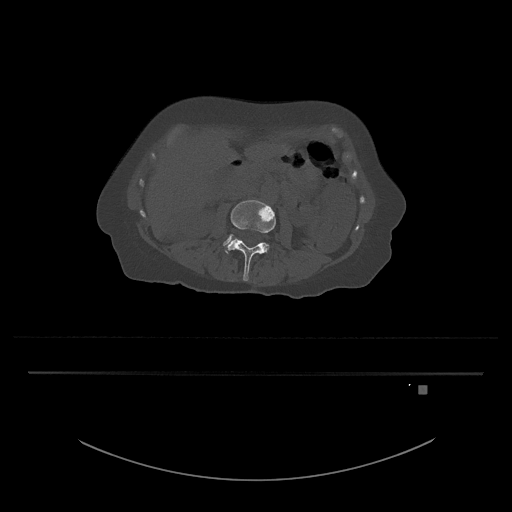
CT including the spine, one axial slice. Slice 419 of 797 in the series (ordered by position). 120 kVp. Bone window (W 1800 / L 400 HU). 0.5 mm slice thickness. 512 × 512 image matrix, field of view 500 × 500 mm. Female patient, age 57 years. From the clinical record (not read from this slice): primary cancer: cervical.
Structures marked on this image (semi-automatic segmentation, software-assisted and operator-edited):
- L3 vertebra: bounding box [x1, y1, x2, y2] px = [225, 200, 276, 281]
- L4 vertebra: [223, 238, 267, 246]